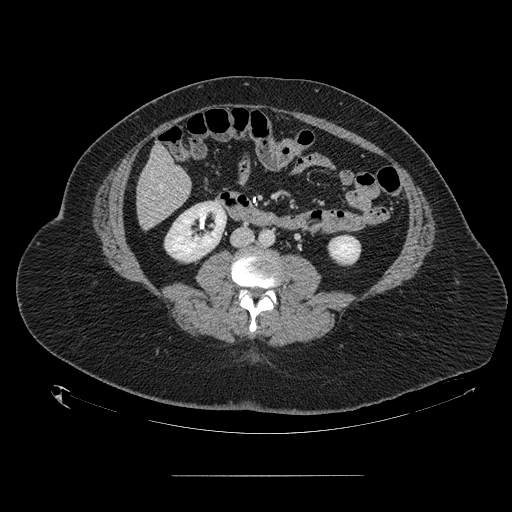
Contrast-enhanced abdominal CT, one axial slice. Position 33 of 164 along the scan axis. 120 kVp. Soft-tissue window (W 400 / L 40 HU). 512 × 512 image matrix, field of view 495 × 495 mm. Female patient, age 52 years. From the clinical record (not read from this slice): diagnosis: colorectal cancer liver metastases, imaged before liver resection; multiple liver metastases: yes; largest metastasis: 3.5 cm.
Outlined on this slice (expert manual segmentation):
- hepatic veins: bounding box <159,185,162,188> (left, top, right, bottom; pixels)
- liver: <138,148,191,229>